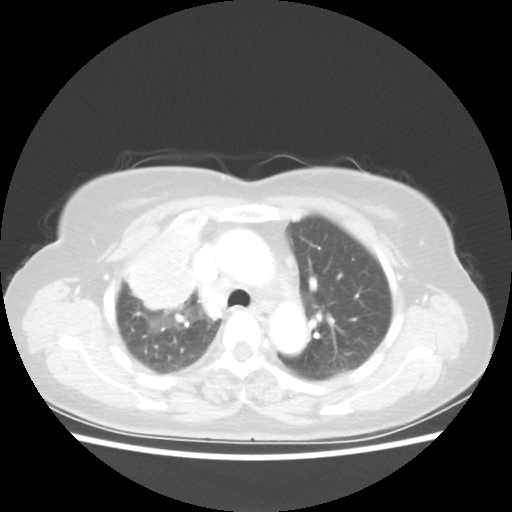
Chest CT, one axial slice; slice 38 of 55 in the series (ordered by position); reconstruction kernel STANDARD; lung window (W 1500 / L -600 HU); 5 mm slice thickness; 512 × 512 image matrix, field of view 337 × 337 mm. Female patient, age 62 years. Case-level facts recorded for this patient, not image findings: clinical TNM (as recorded): T4 N3 M0.
Annotated regions visible in this slice (rectangle marked by the reading radiologist):
- lung tumour (recorded histology: squamous cell carcinoma): bounding box [x1, y1, x2, y2] px = [116, 203, 211, 322]